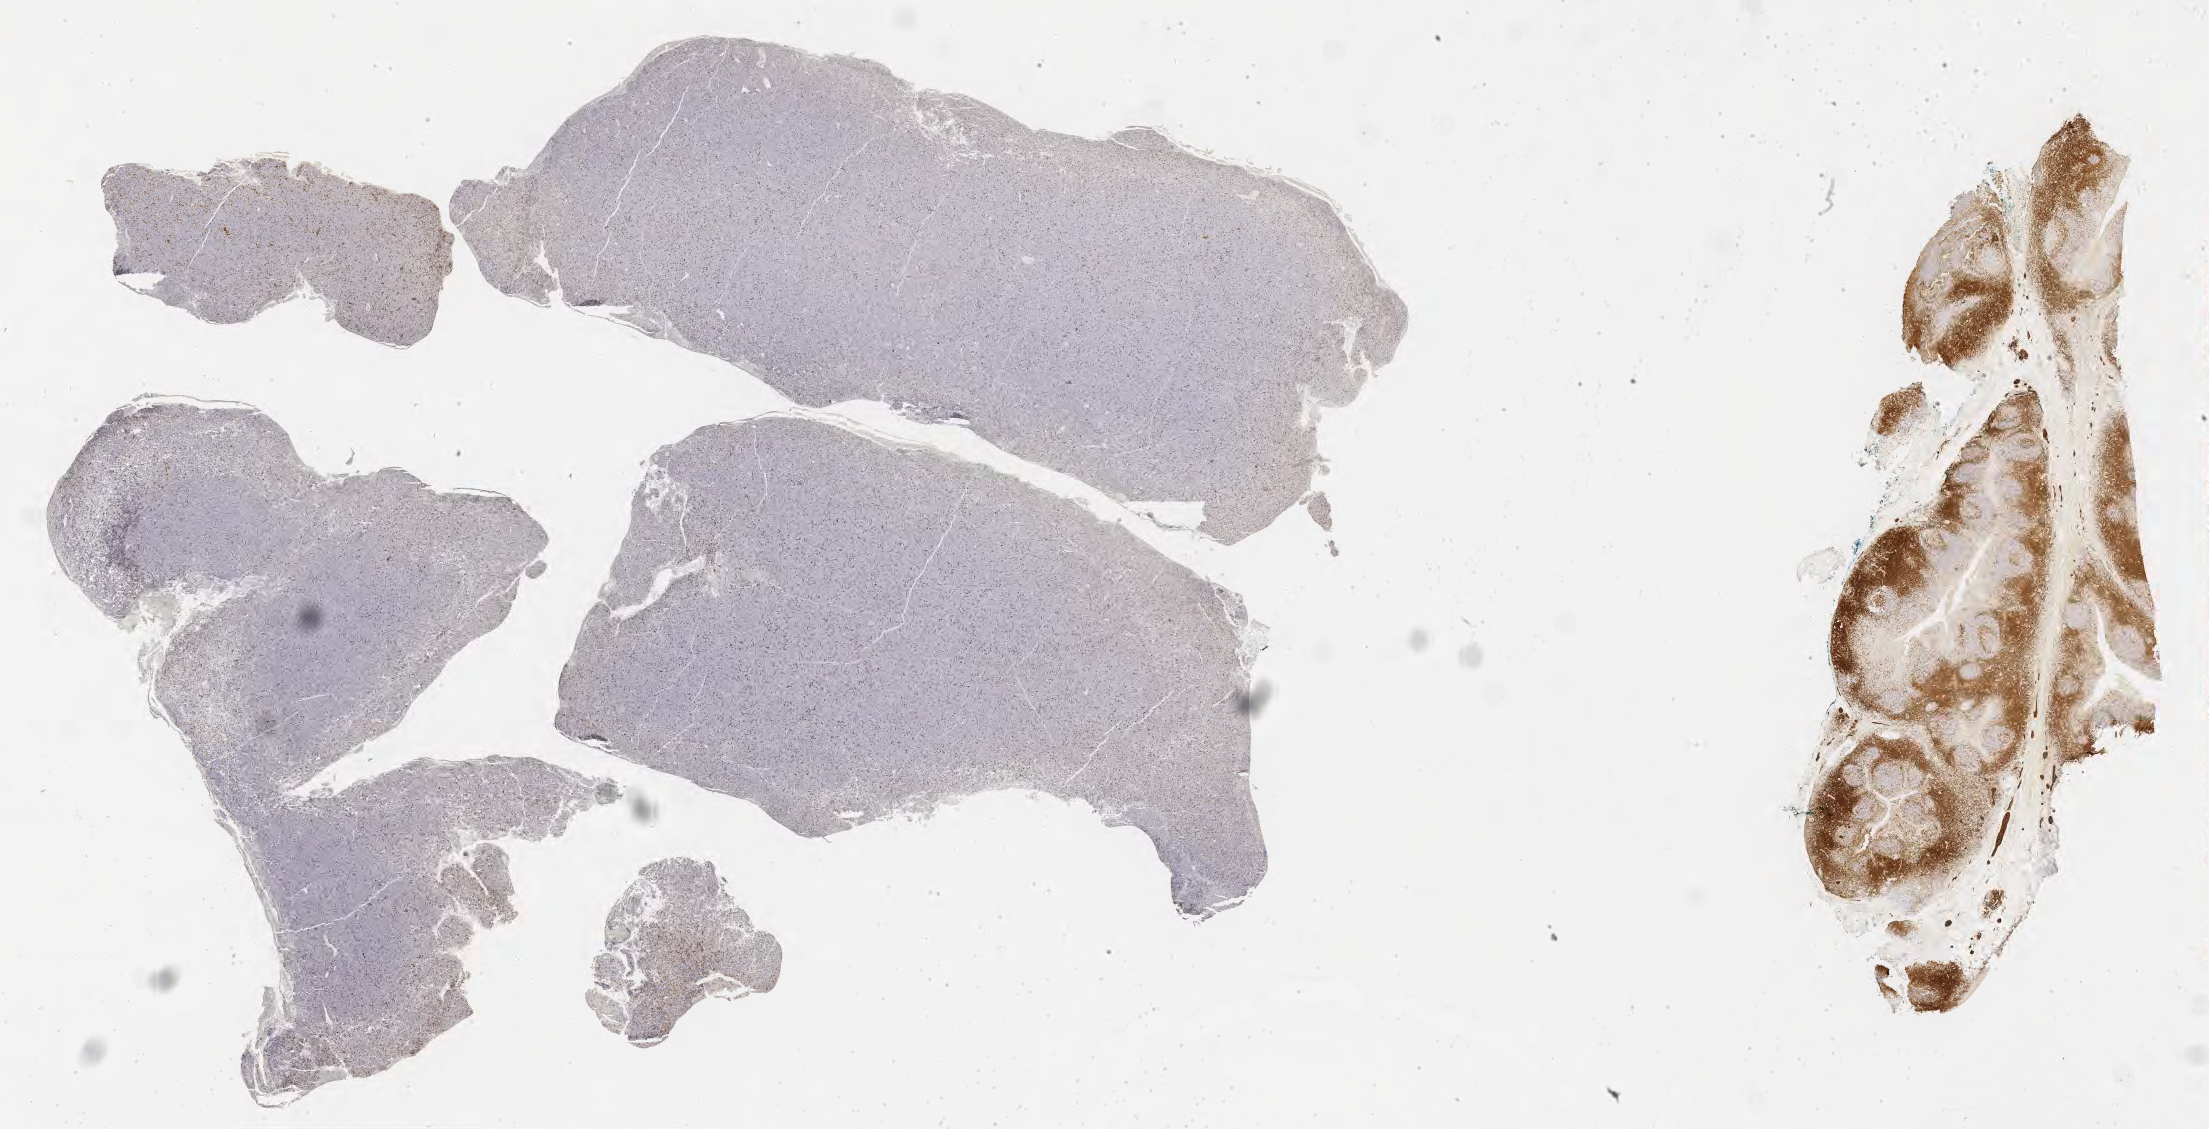
Whole-slide image, immunohistochemical stain for CD3, a low-resolution overview of the entire scanned area, about 35.7 x 18.3 mm. Specimen: tumor tissue. Anatomic site: peritoneum. Patient: female, age at initial diagnosis 7 years.
* histologic diagnosis: Burkitt lymphoma, NOS